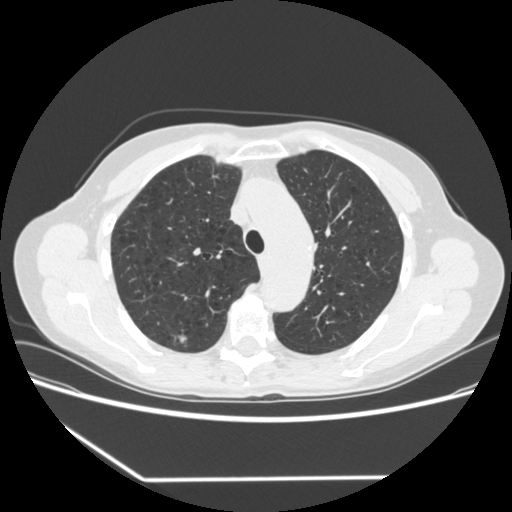
Low-dose screening chest CT, one axial slice; slice 249 of 323 in the series (ordered by position); reconstruction kernel STANDARD; lung window (W 1500 / L -600 HU); 1.25 mm slice thickness; 512 × 512 image matrix, field of view 360 × 360 mm.
Structures marked on this image (manually delineated by an expert):
- lesion 1 (tumor, upper lobe of right lung): bounding box (x1, y1, x2, y2) in pixels: (178, 336, 187, 354)